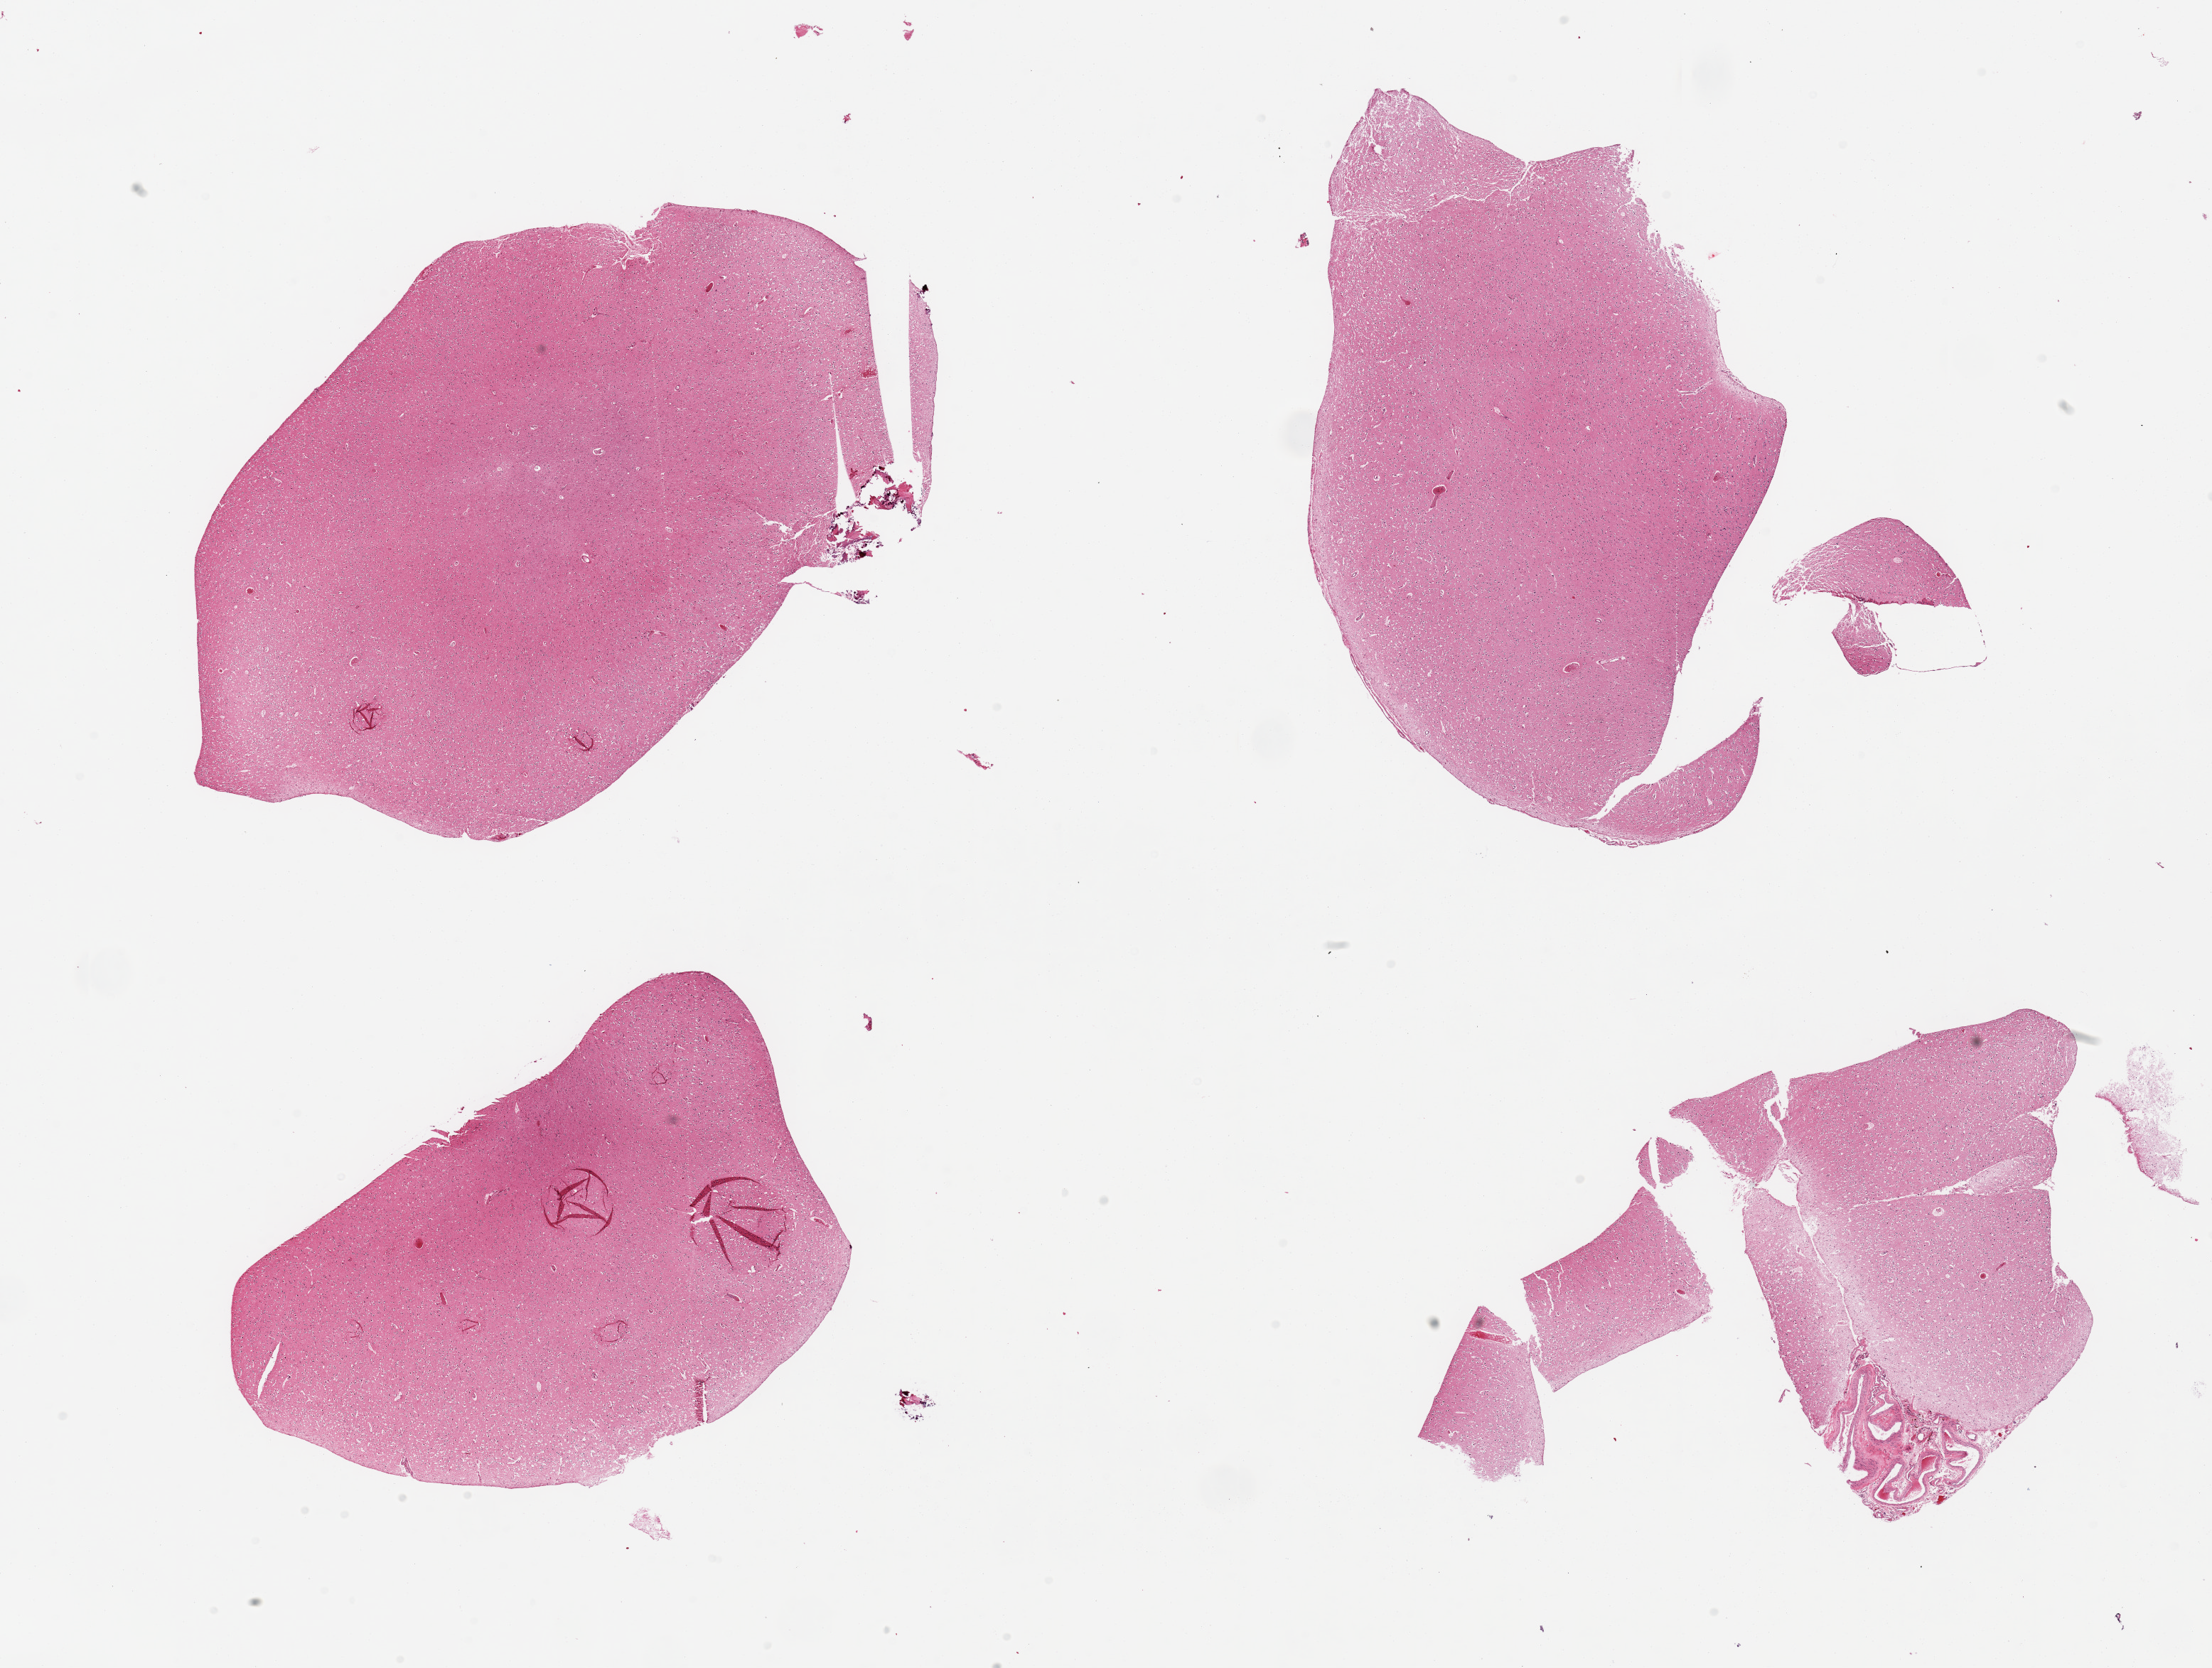
Whole-slide image, H&E stain — shown as a low-resolution overview of the whole scanned area (about 24.6 x 18.6 mm, from a 20x scan); PAXgene-fixed paraffin-embedded (PFPE) section; target tissue: cerebral cortex; donor tissue sample. Donor: male.
Pathologist's review note for this sample: 4 fragmented pieces; mild to moderate autolysis; attached small fragments of meninges.